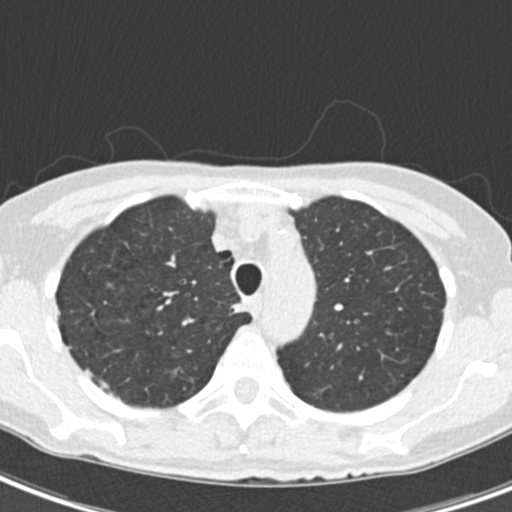
Axial slice from a low-dose chest CT screening exam. Second annual screen. Lung window (W 1500 / L -600 HU). 2 mm slice thickness. Slice 46 of 218 in the series. 512 × 512 image matrix, field of view 286 × 286 mm. Female participant, aged 68 years at enrolment. Current smoker at enrolment.
- Lesion marked by an expert reader, bounding box [x1, y1, x2, y2] px = [226, 300, 253, 324].
- Screening reader's record for this exam: no non-calcified nodule ≥4 mm recorded.
- Later outcome: lung cancer diagnosed 436 days after this screen (after the third annual screen) — squamous cell carcinoma, NOS, right upper lobe, mediastinum, poorly differentiated (G3), stage IIIB (AJCC 6th edition), 43 mm at pathology.